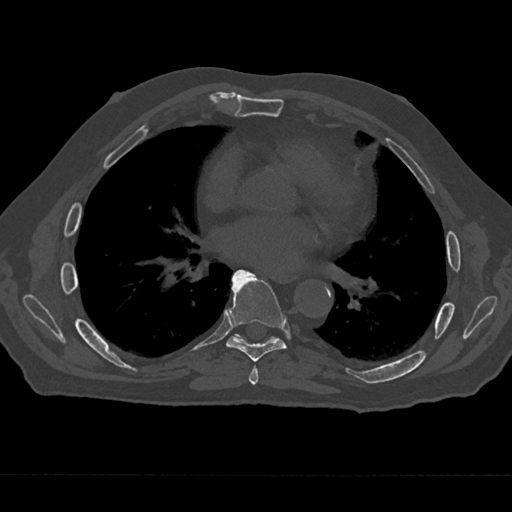
CT including the spine, one axial slice; position 363 of 797 along the scan axis; reconstruction kernel Br40s/3; bone window (W 1800 / L 400 HU); 512 × 512 image matrix. Patient: male, 75 years. From the clinical record (not read from this slice): primary cancer: renal; vertebrae with lytic lesions (as recorded): T4.
Outlined on this slice (semi-automatic segmentation, software-assisted and operator-edited):
- T6 vertebra: bounding box [x1, y1, x2, y2] px = [249, 366, 259, 385]
- T7 vertebra: [227, 269, 287, 362]
- T8 vertebra: [235, 334, 275, 340]